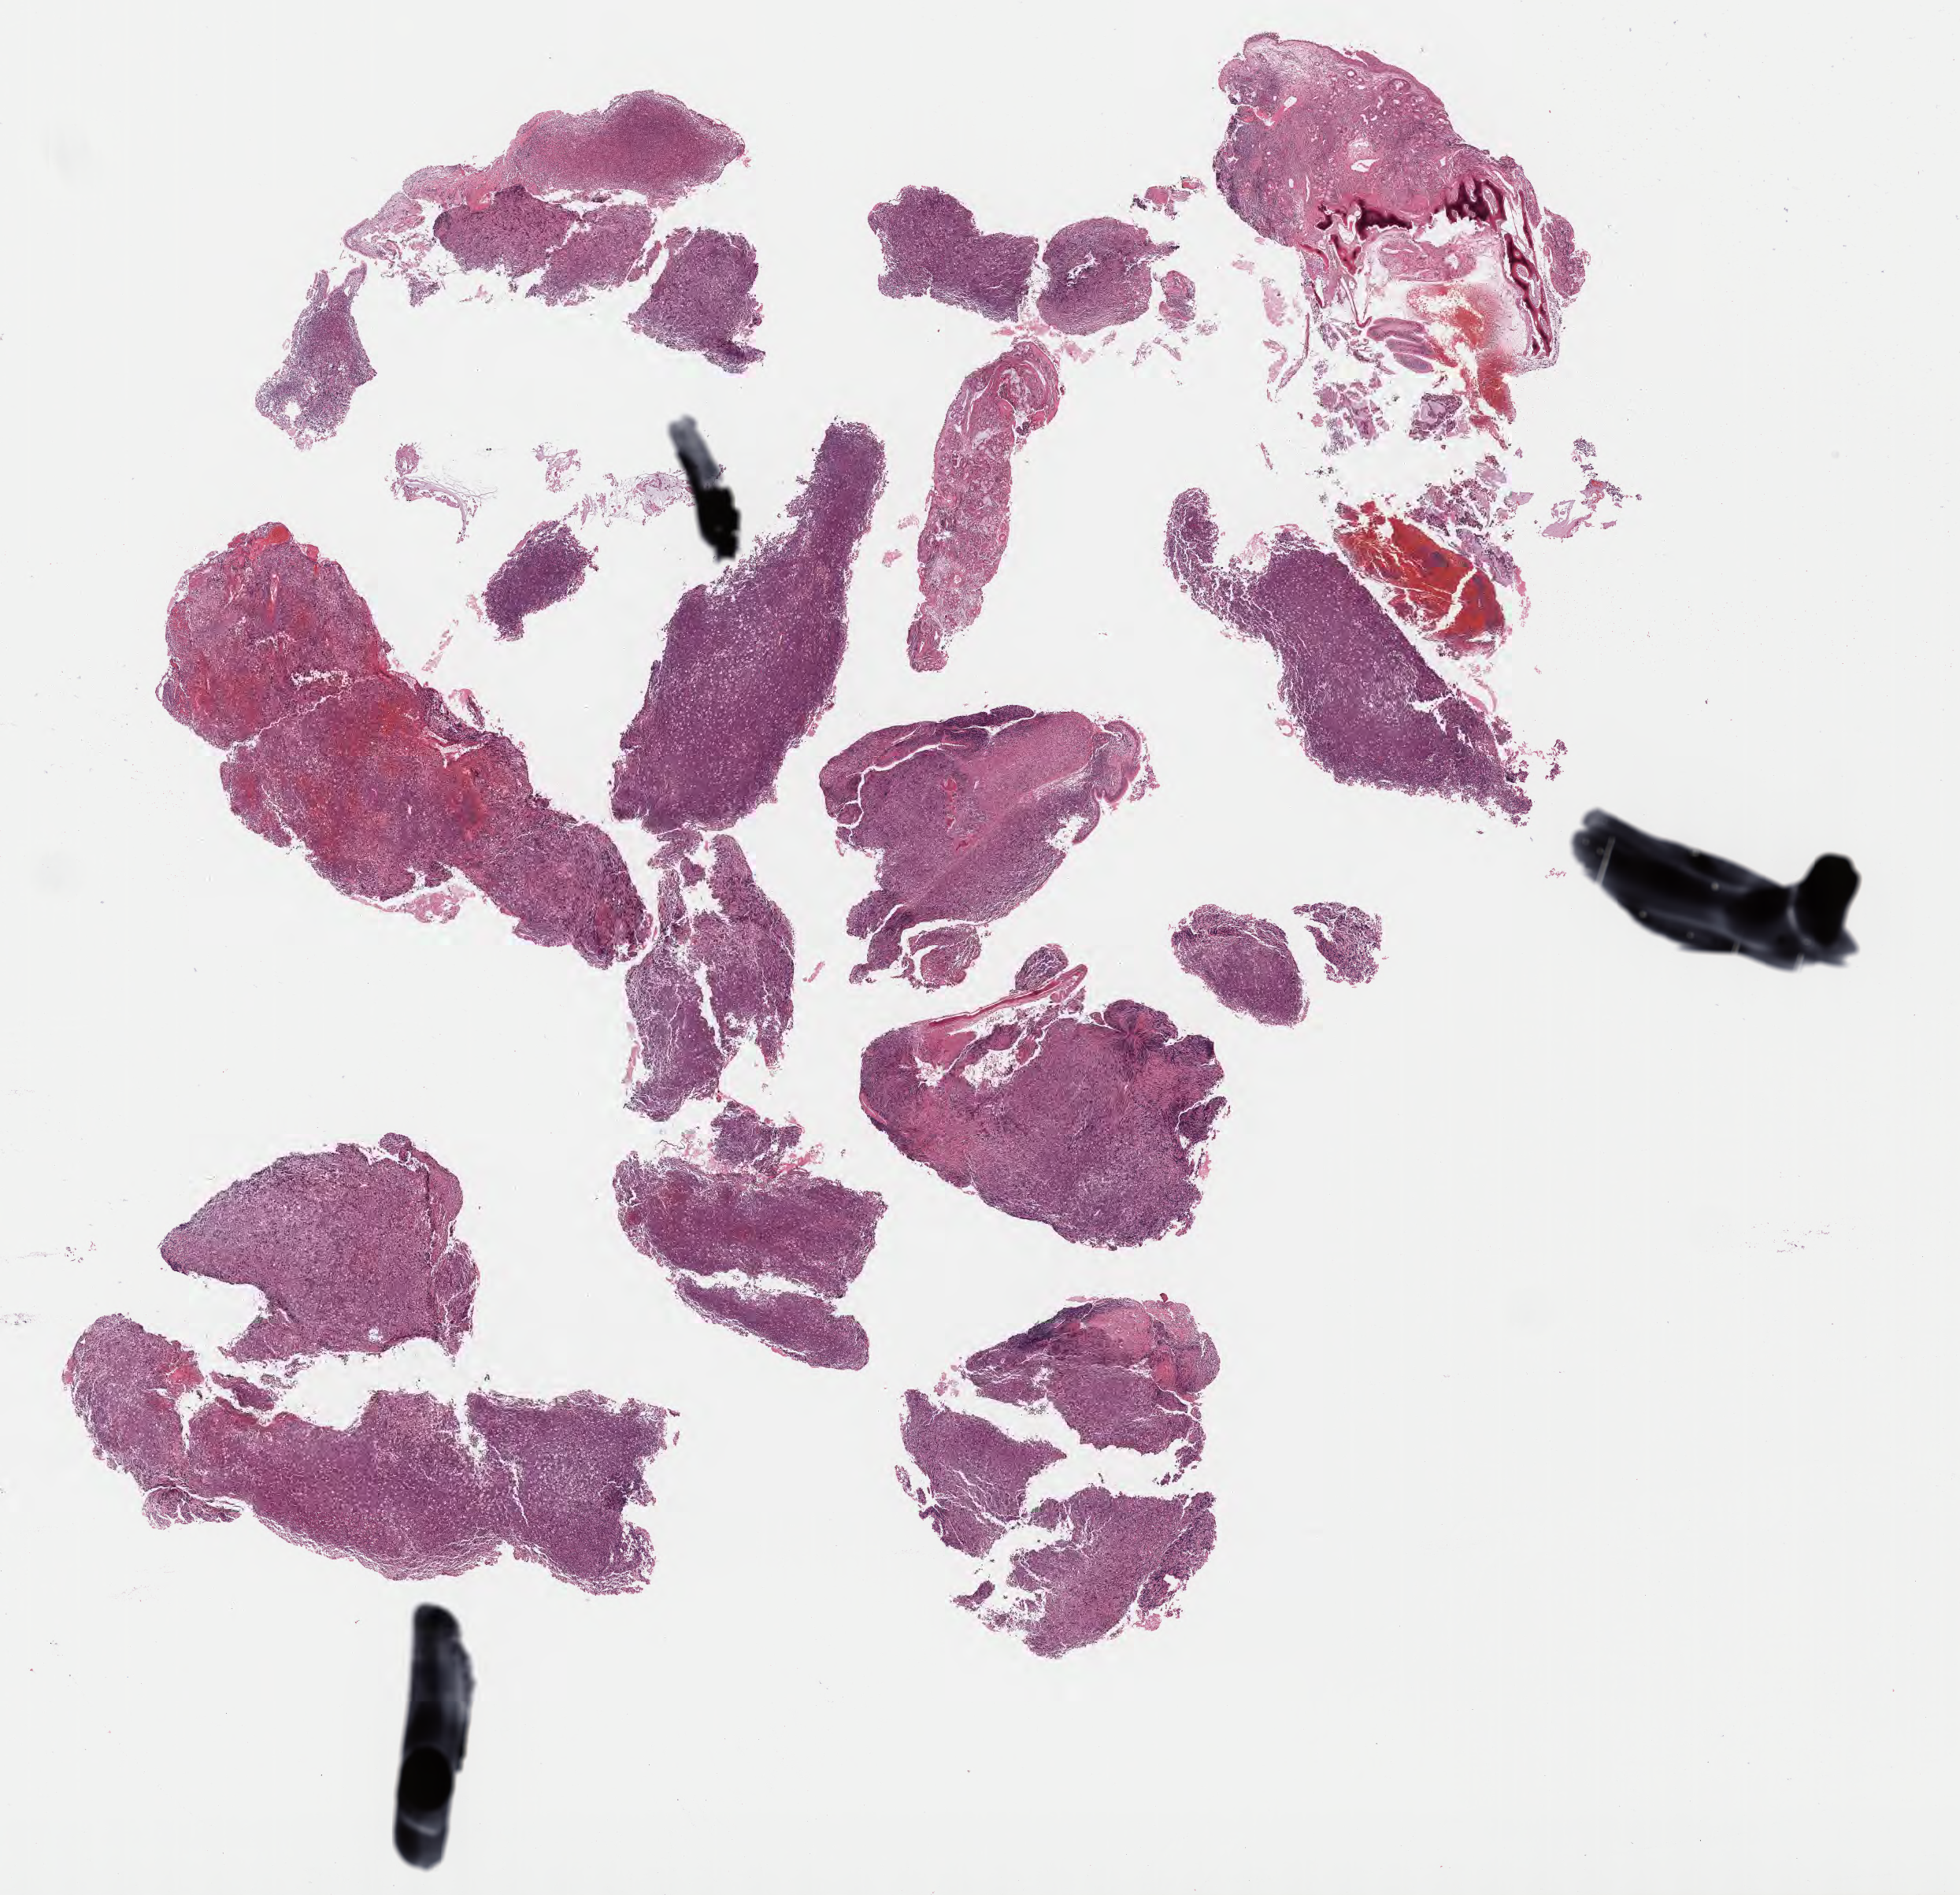
Digitized hematoxylin and eosin (H&E)-stained section — shown as a low-resolution overview of the whole scanned area (about 20.1 x 19.5 mm). Tumor tissue. Male patient, 38 years old.
- diagnosis: Burkitt lymphoma, NOS